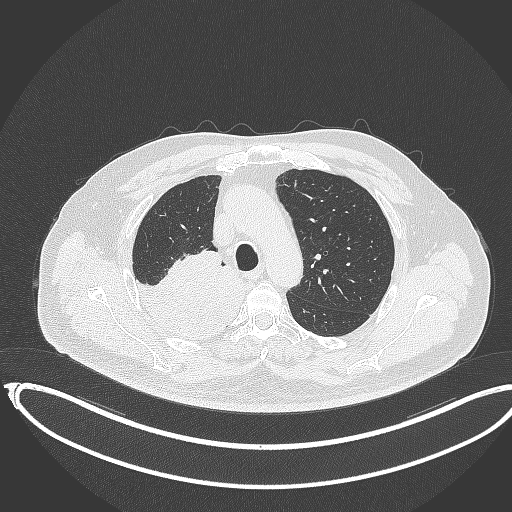
Chest CT, one axial slice. Position 267 of 403 along the scan axis. Reconstruction kernel B70f. 120 kVp. Lung window (W 1500 / L -600 HU). 1 mm slice thickness. 512 × 512 image matrix, field of view 436 × 436 mm. Patient: male, 68 years. From the clinical record (not read from this slice): clinical TNM (as recorded): T2a N0 M0.
Annotated regions visible in this slice (rectangle marked by the reading radiologist):
- lung tumour (recorded histology: adenocarcinoma): bounding box [x1, y1, x2, y2] px = [131, 253, 249, 339]